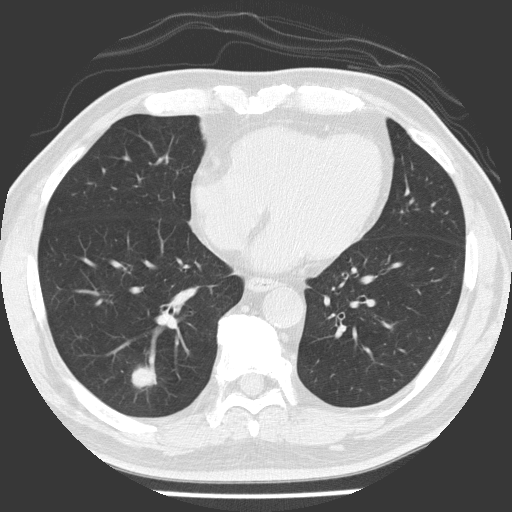
Low-dose screening chest CT, axial slice. First (baseline) screen. Lung window (W 1500 / L -600 HU). 2 mm slice thickness. Lung (sharp) reconstruction kernel (FC51). Slice 94 of 154 in the series. 512 × 512 image matrix. Male, age 56 years at enrolment.
Expert reader's lesion annotation, bounding box [x1, y1, x2, y2] px = [109, 345, 165, 404]. The exam's reader record, not a measurement of the box and not confirmed to be the same lesion: non-calcified nodule or mass ≥4 mm, right lower lobe, 21 × 17 mm, spiculated (stellate) margins, soft tissue attenuation. Official screen result: positive, change unspecified: nodule(s) >= 4 mm or enlarging nodule(s), mass(es), or other non-specific abnormalities suspicious for lung cancer. Lung cancer was diagnosed 84 days after this screen: adenocarcinoma, NOS, right lower lobe, poorly differentiated (G3), stage IA (AJCC 6th edition), 24 mm at pathology.